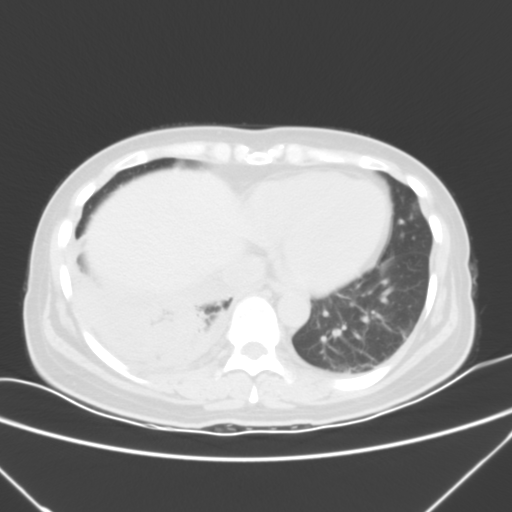
Chest CT, one axial slice. Slice 13 of 53 in the series (ordered by position). 120 kVp. Lung window (W 1500 / L -600 HU). 5 mm slice thickness. 512 × 512 image matrix. Patient: female, 42 years. From the clinical record (not read from this slice): clinical TNM (as recorded): T3 N0 M1c.
Annotated regions visible in this slice (bounding box drawn by a radiologist):
- lung tumour (recorded histology: adenocarcinoma): bounding box [x1, y1, x2, y2] px = [76, 274, 210, 372]